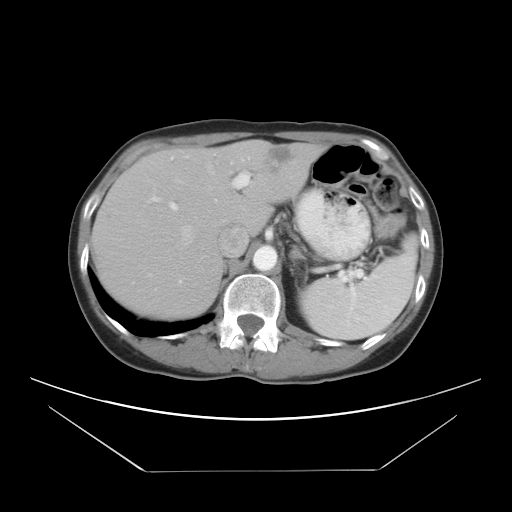
Contrast-enhanced abdominal CT, one axial slice; slice 20 of 30 in the series (ordered by position); reconstruction kernel STANDARD; 120 kVp; intravenous contrast given; soft-tissue window (W 400 / L 40 HU); 7.5 mm slice thickness; 512 × 512 image matrix. Female patient, age 54 years. From the clinical record (not read from this slice): diagnosis: colorectal cancer liver metastases, imaged before liver resection; multiple liver metastases: yes; largest metastasis: 2.5 cm; chemotherapy before resection: no.
Outlined on this slice (outlined manually by an expert reader):
- hepatic veins: bounding box [x1, y1, x2, y2] px = [147, 165, 215, 291]
- liver: [94, 142, 320, 317]
- planned liver remnant (the part of the liver to remain after resection): [94, 147, 267, 317]
- portal vein (with intrahepatic branches): [147, 154, 249, 211]
- liver metastasis: [265, 148, 295, 173]